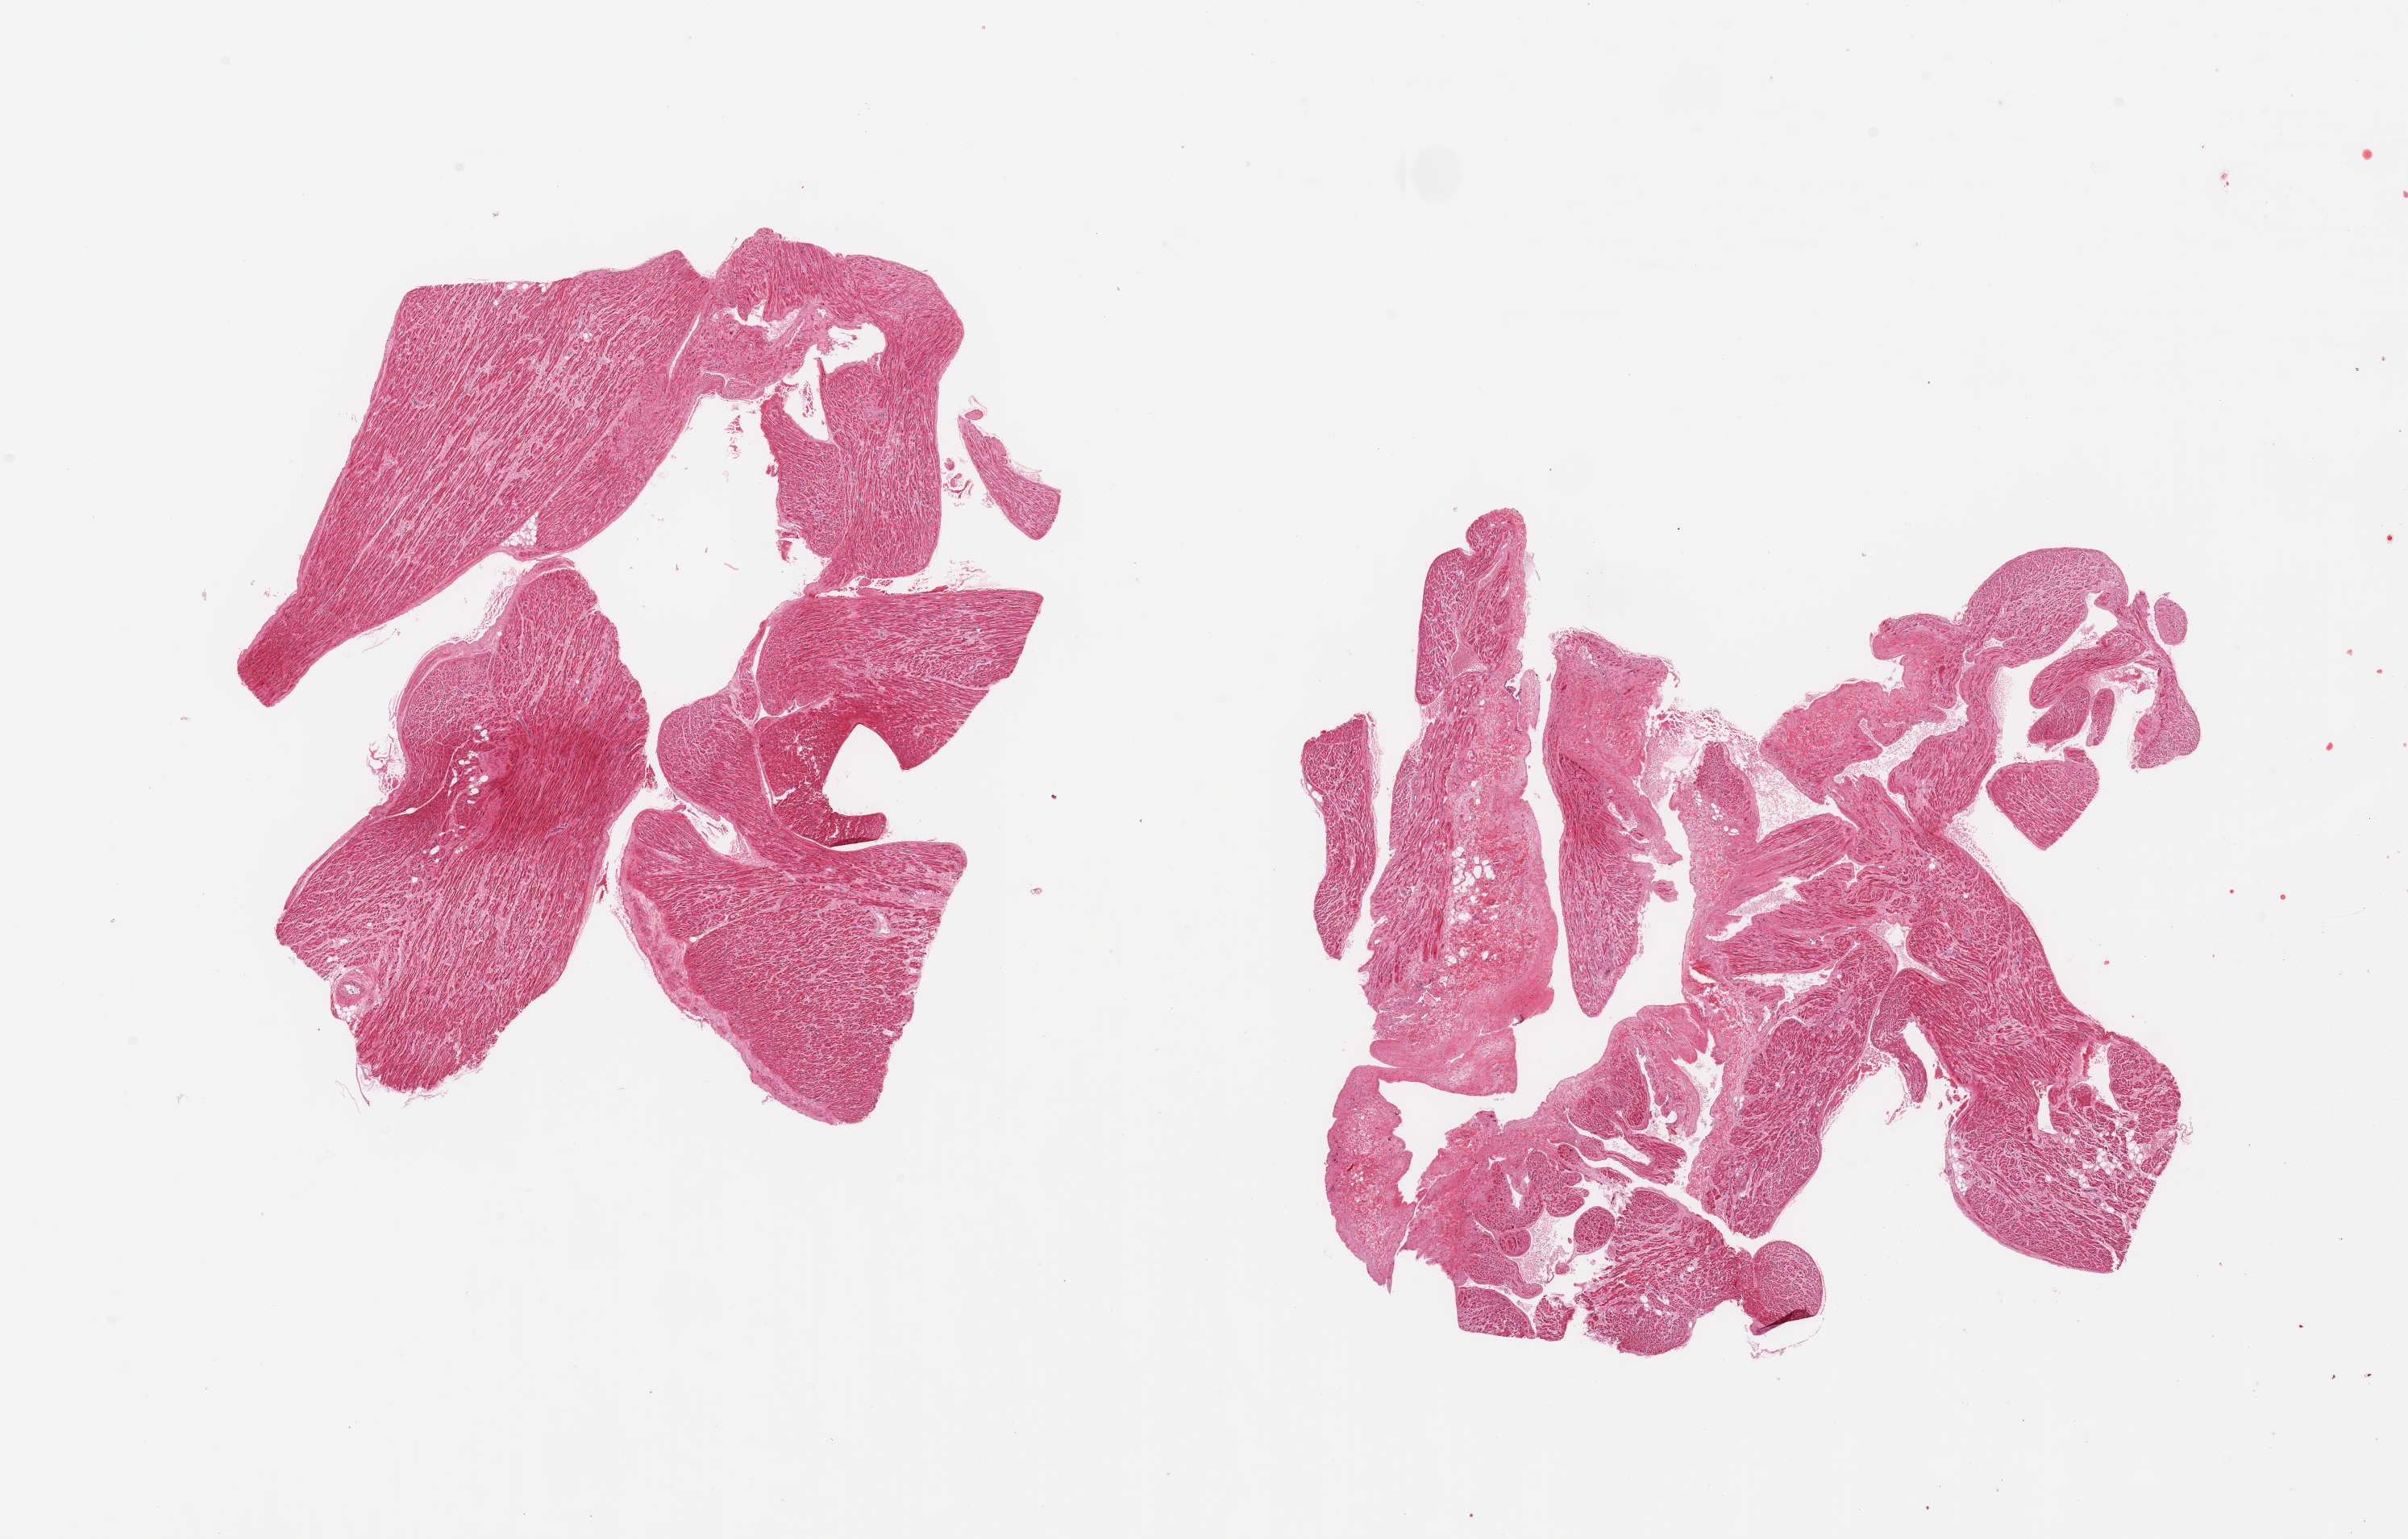
Haematoxylin and eosin whole-slide image, brightfield — a low-resolution overview of the entire scanned area, about 23.6 x 15.1 mm (from a 20x scan); PAXgene-fixed paraffin-embedded (PFPE) section; target tissue: auricular appendage; tissue donor sample.
Reviewer comment on this tissue sample: 2 pieces; up to 20% is fibrous, trivial internal fat.